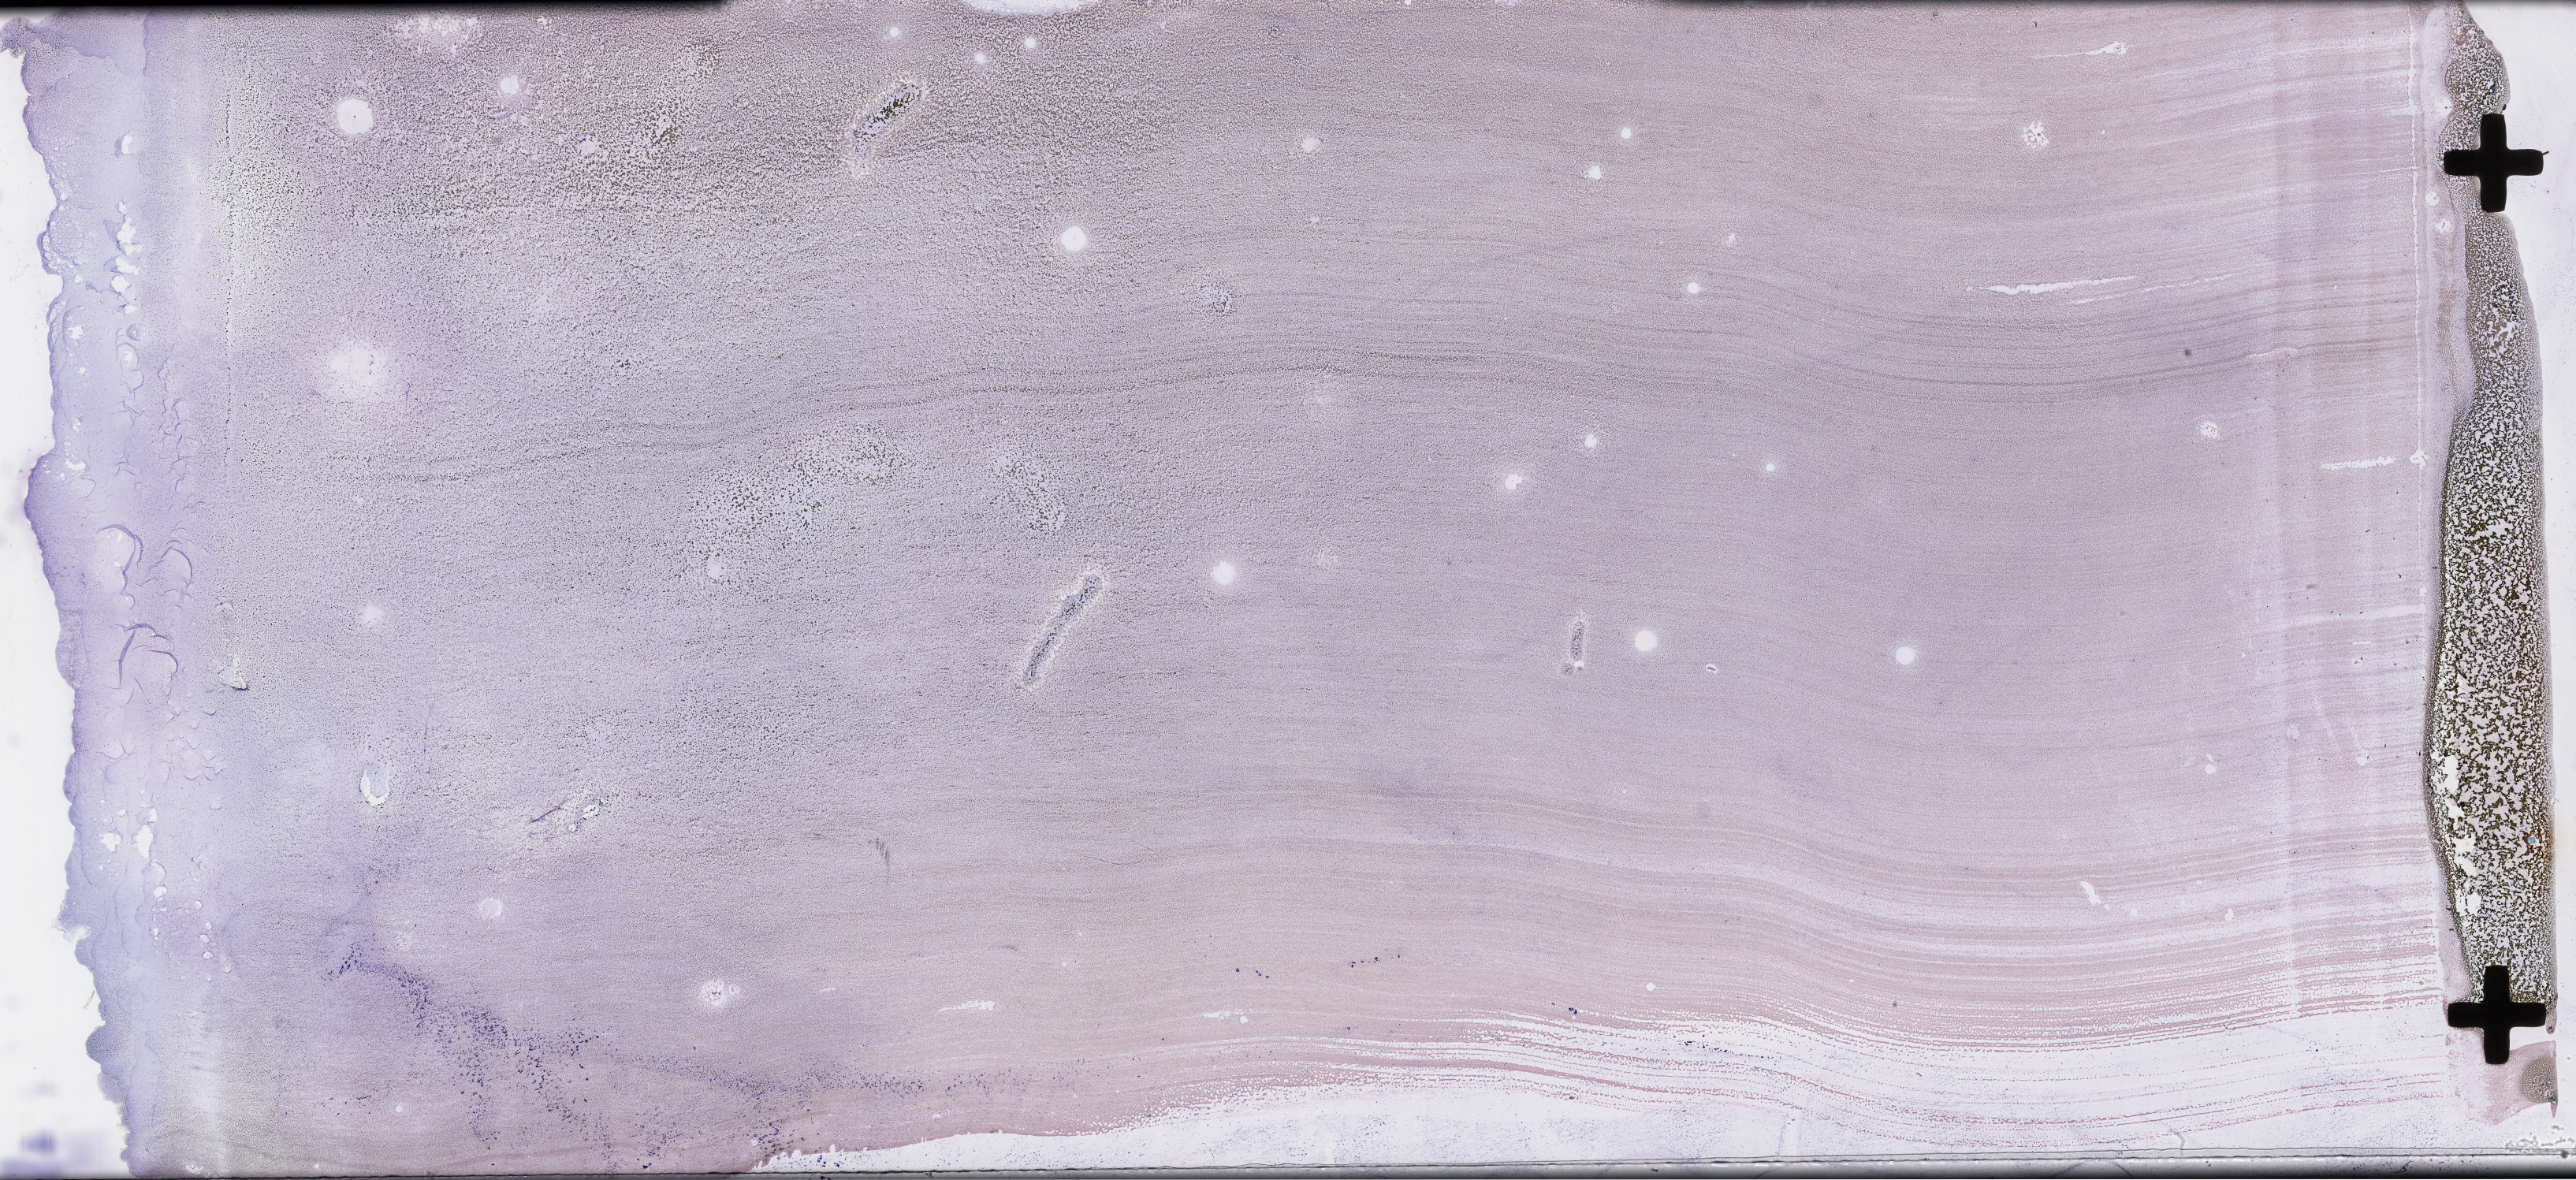
Whole-slide image of a bone marrow smear, Wright–Giemsa stain, shown as a low-resolution overview of the whole scanned area (about 52.8 x 24.2 mm). Male patient.
Patient diagnosis: Plasma Cell Myeloma.